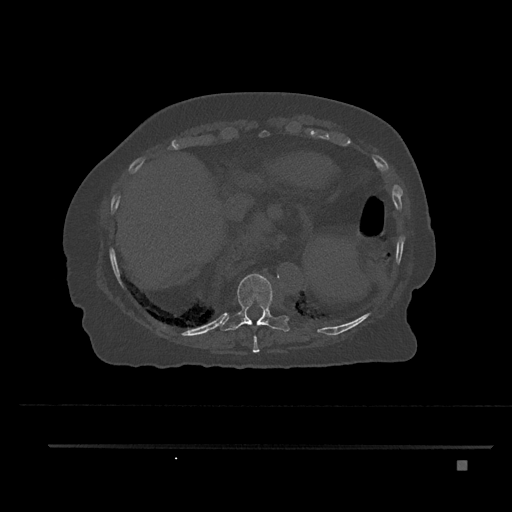
CT including the spine, one axial slice; position 362 of 797 along the scan axis; 120 kVp; bone window (W 1800 / L 400 HU); 0.5 mm slice thickness; 512 × 512 image matrix, field of view 437 × 437 mm. Female patient, age 76 years. From the clinical record (not read from this slice): primary cancer: lung; vertebrae with lytic lesions (as recorded): T11, L3.
Annotated regions visible in this slice (semi-automatically segmented with operator editing):
- T10 vertebra: bounding box (x1, y1, x2, y2) in pixels: (220, 273, 290, 332)
- T9 vertebra: (253, 335, 260, 353)